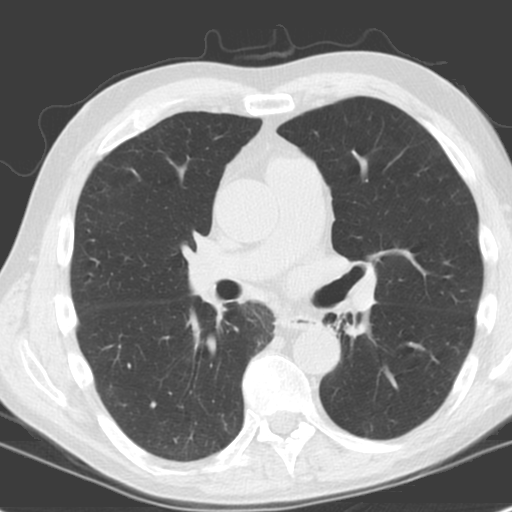
Chest CT (low-dose screening protocol), one axial image; first (baseline) screen; lung window (W 1500 / L -600 HU); 3.2 mm slice thickness; standard (soft-tissue) reconstruction kernel (C); 120 kVp; 512 × 512 image matrix, field of view 321 × 321 mm. Male, age 61 years at enrolment. Former smoker at enrolment.
• Lesion marked by an expert reader, bounding box (x1, y1, x2, y2) in pixels: (313, 309, 365, 345).
• Screening reader's record for this exam: no non-calcified nodule ≥4 mm recorded.
• Participant outcome: lung cancer diagnosed 1146 days after this screen (after the third annual screen) — squamous cell carcinoma, NOS, left upper lobe, left lower lobe, well differentiated (G1), stage IIB (AJCC 6th edition), 100 mm at pathology.